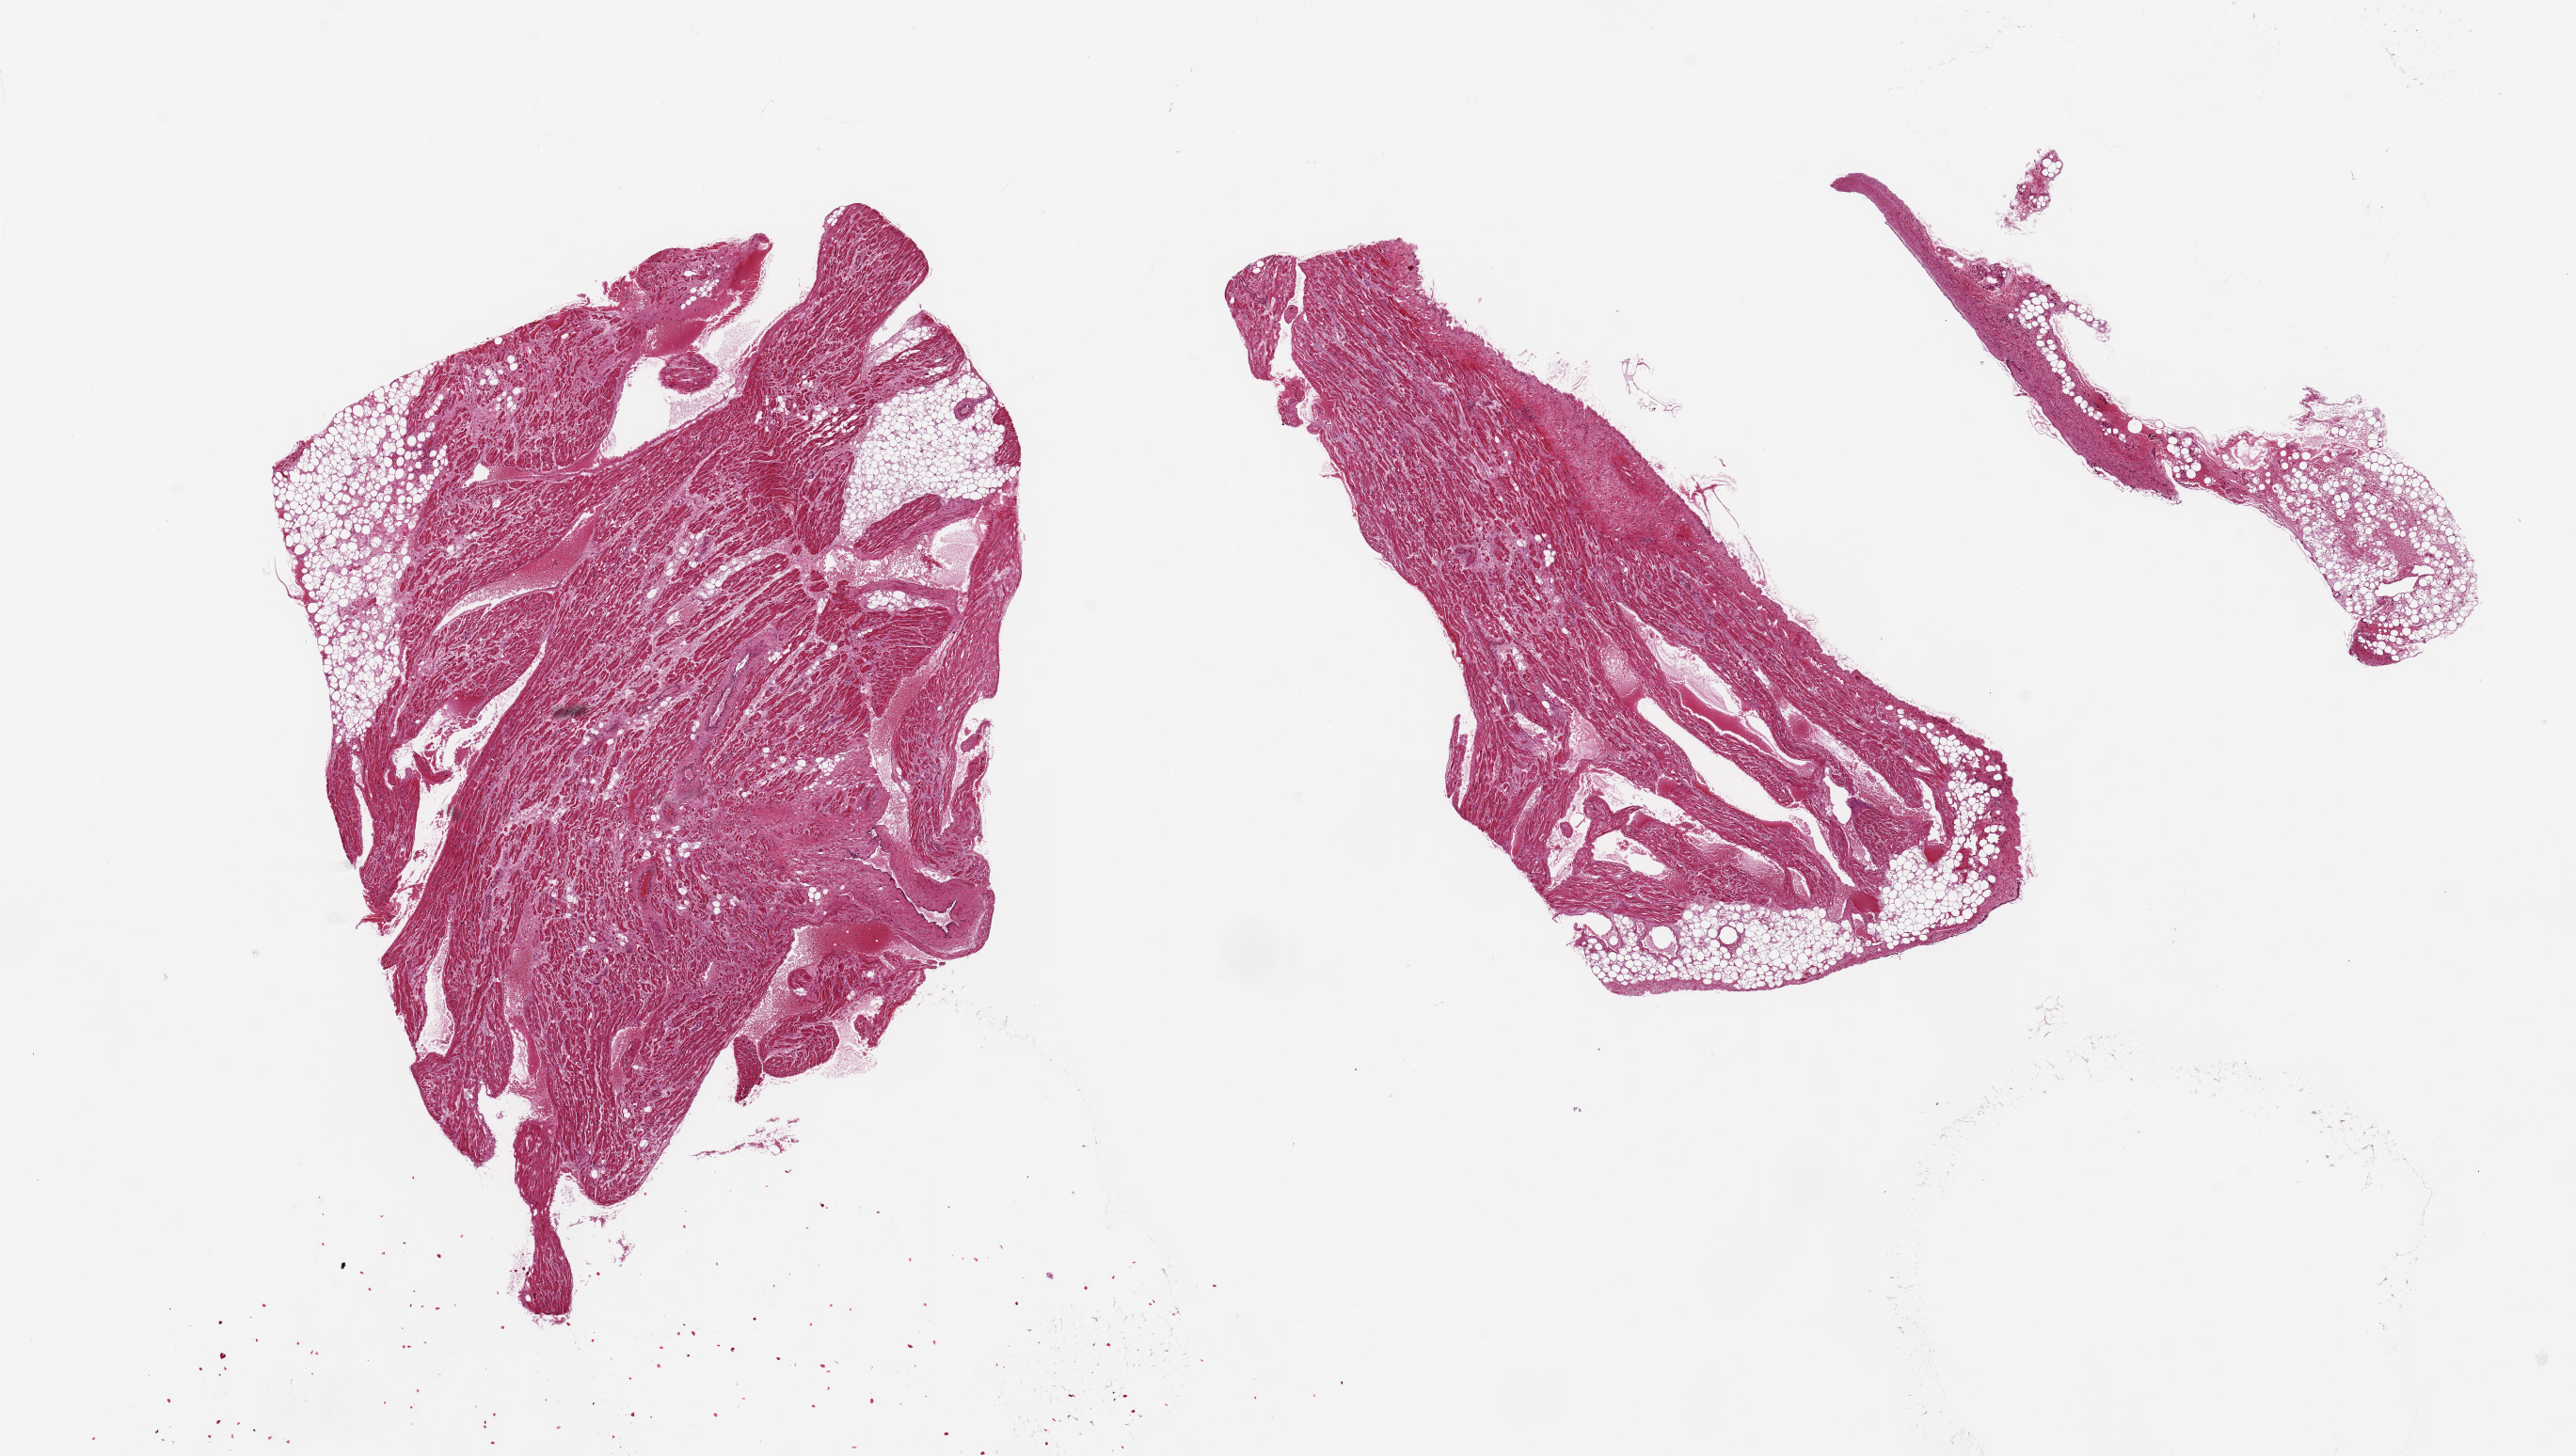
Digitized H&E-stained section — shown as a low-resolution overview of the whole scanned area (about 21.7 x 12.2 mm, acquisition: 20x scan), PAXgene-fixed paraffin-embedded (PFPE) section, section of auricular appendage (target tissue), tissue donor sample.
Pathologist's review note for this sample: 2 pieces, 8x7 & 8x8mm.